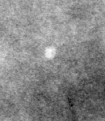
Region of interest cut from a scanned film mammogram (one marked finding), right breast, CC view.
Calcifications, morphology round and regular / lucent centered; BI-RADS assessment category 2; benign; no additional work-up was recommended (benign without callback).